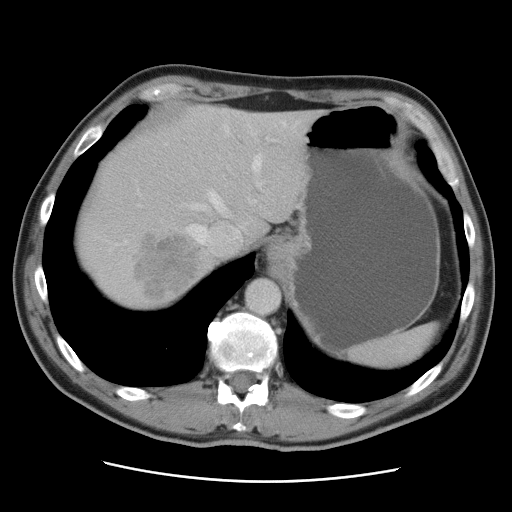
Contrast-enhanced abdominal CT, one axial slice. Slice 73 of 89 in the series (ordered by position). Intravenous contrast given. Soft-tissue window (W 400 / L 40 HU). 5 mm slice thickness. 512 × 512 image matrix, field of view 366 × 366 mm. Male patient, age 59 years. Case-level facts recorded for this patient, not image findings: diagnosis: colorectal cancer liver metastases, imaged before liver resection; multiple liver metastases: yes; largest metastasis: 0.6 cm; disease in both lobes: yes.
Annotated regions visible in this slice (expert manual segmentation):
- hepatic veins: bounding box [x1, y1, x2, y2] px = [138, 122, 298, 256]
- liver: [74, 107, 322, 312]
- planned liver remnant (the part of the liver to remain after resection): [121, 107, 322, 245]
- portal vein (with intrahepatic branches): [267, 138, 275, 141]
- liver metastasis: [136, 236, 201, 302]